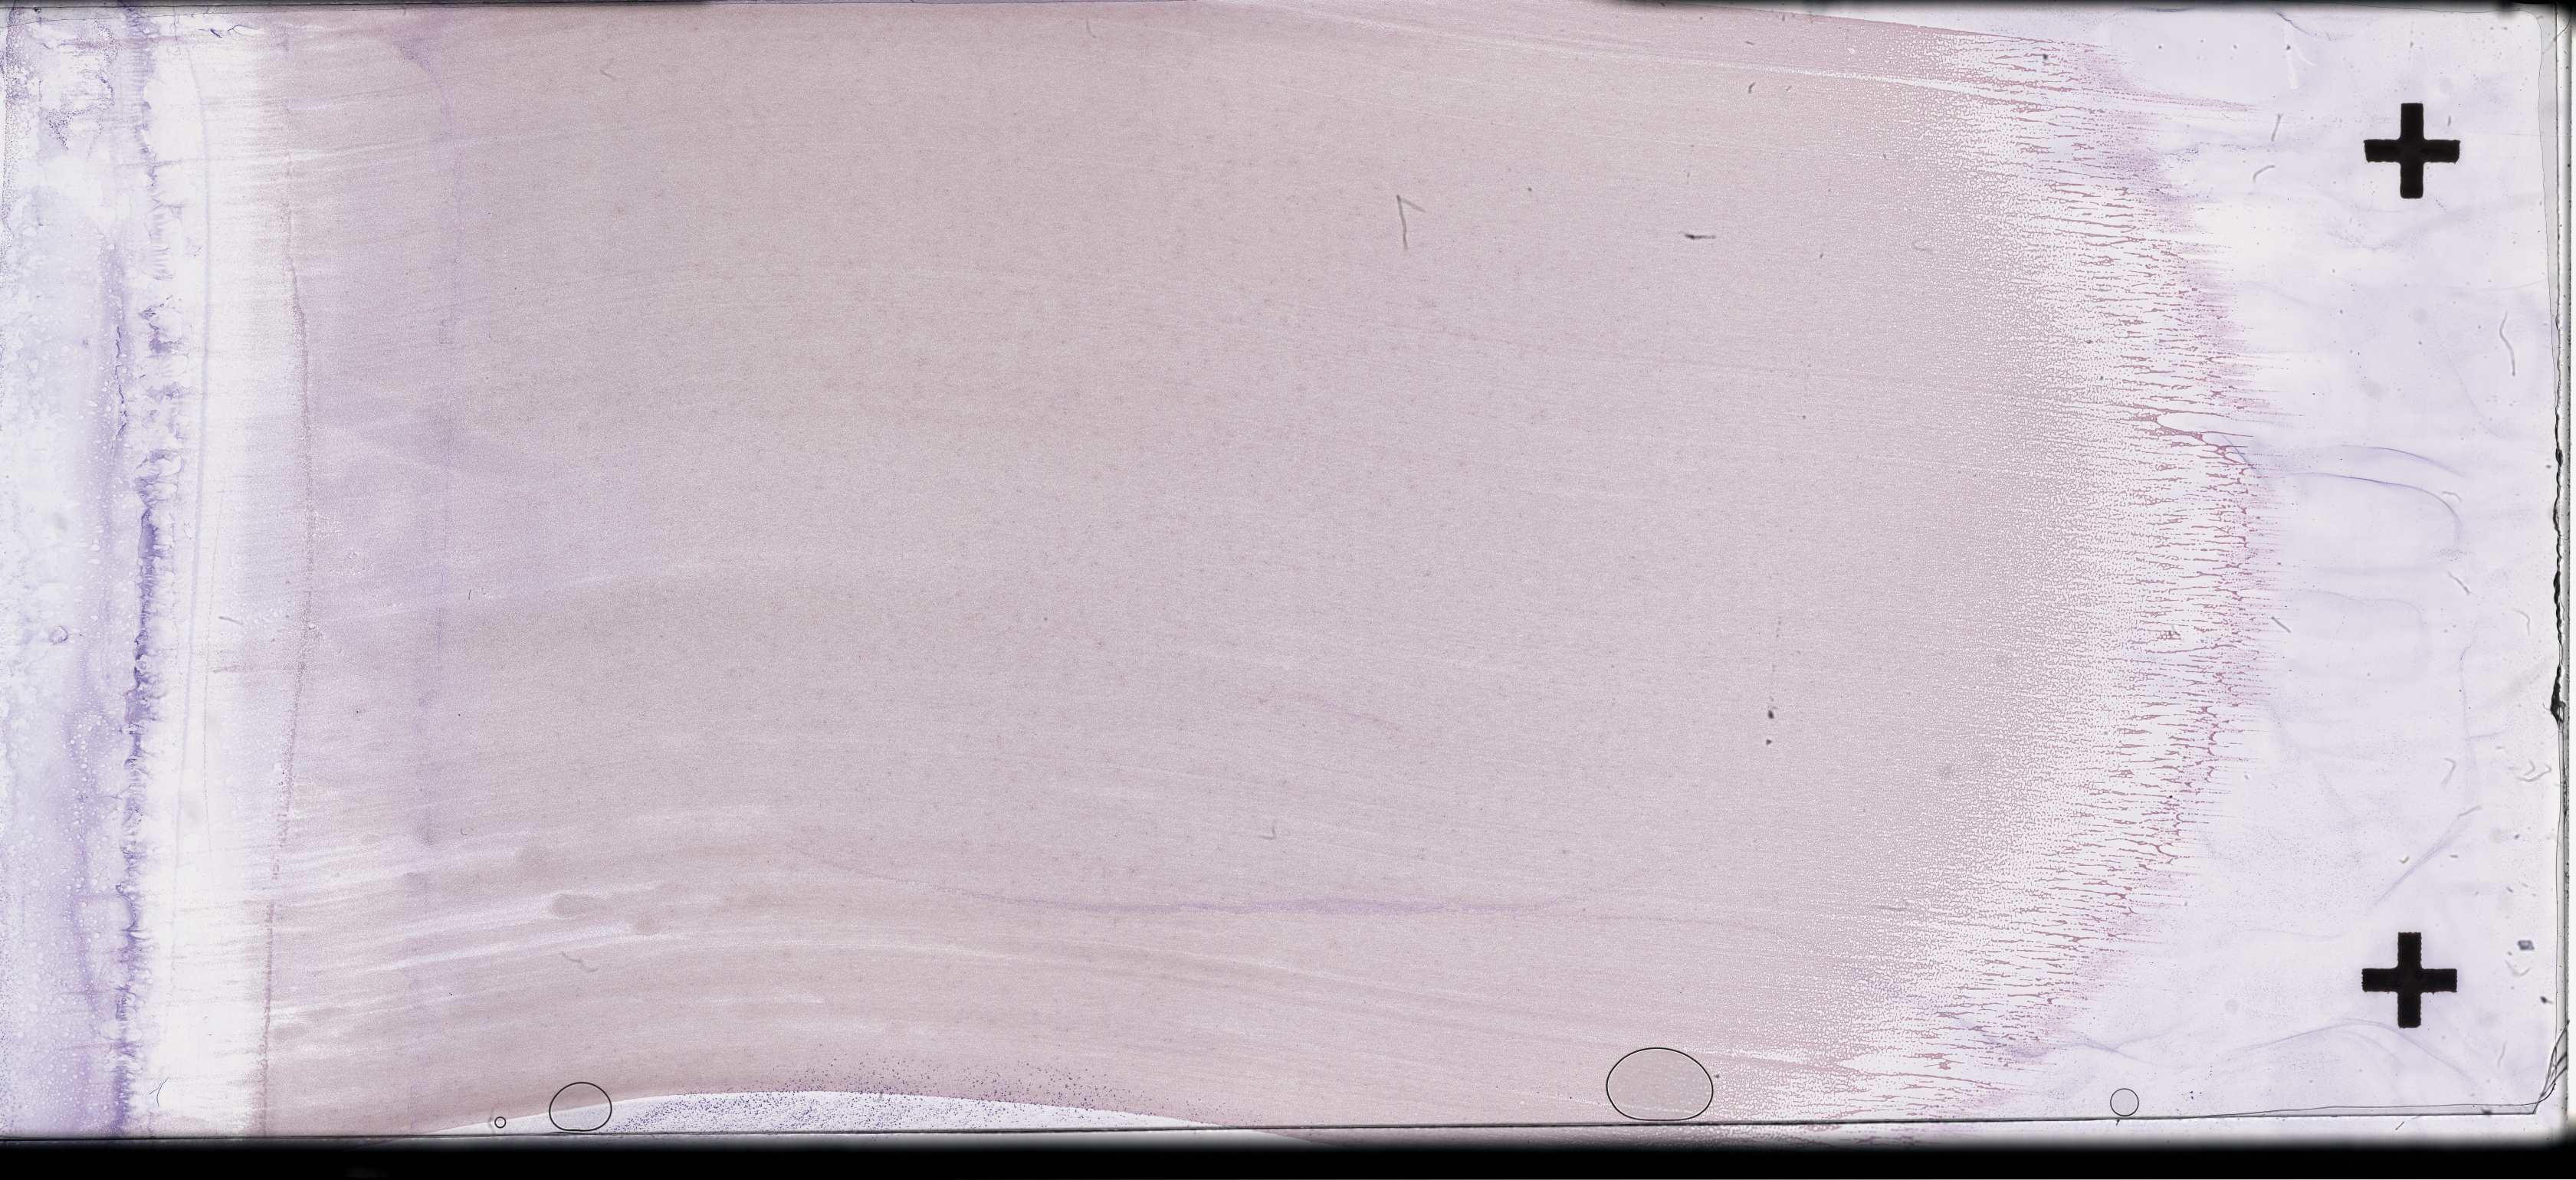
Whole-slide image of a whole blood smear, Wright-Giemsa stain — low-resolution overview of the scanned area, about 54.3 x 24.9 mm. Smear from an EDTA sample. Collected on treatment. Patient: female.
Patient diagnosis: Plasma Cell Myeloma.